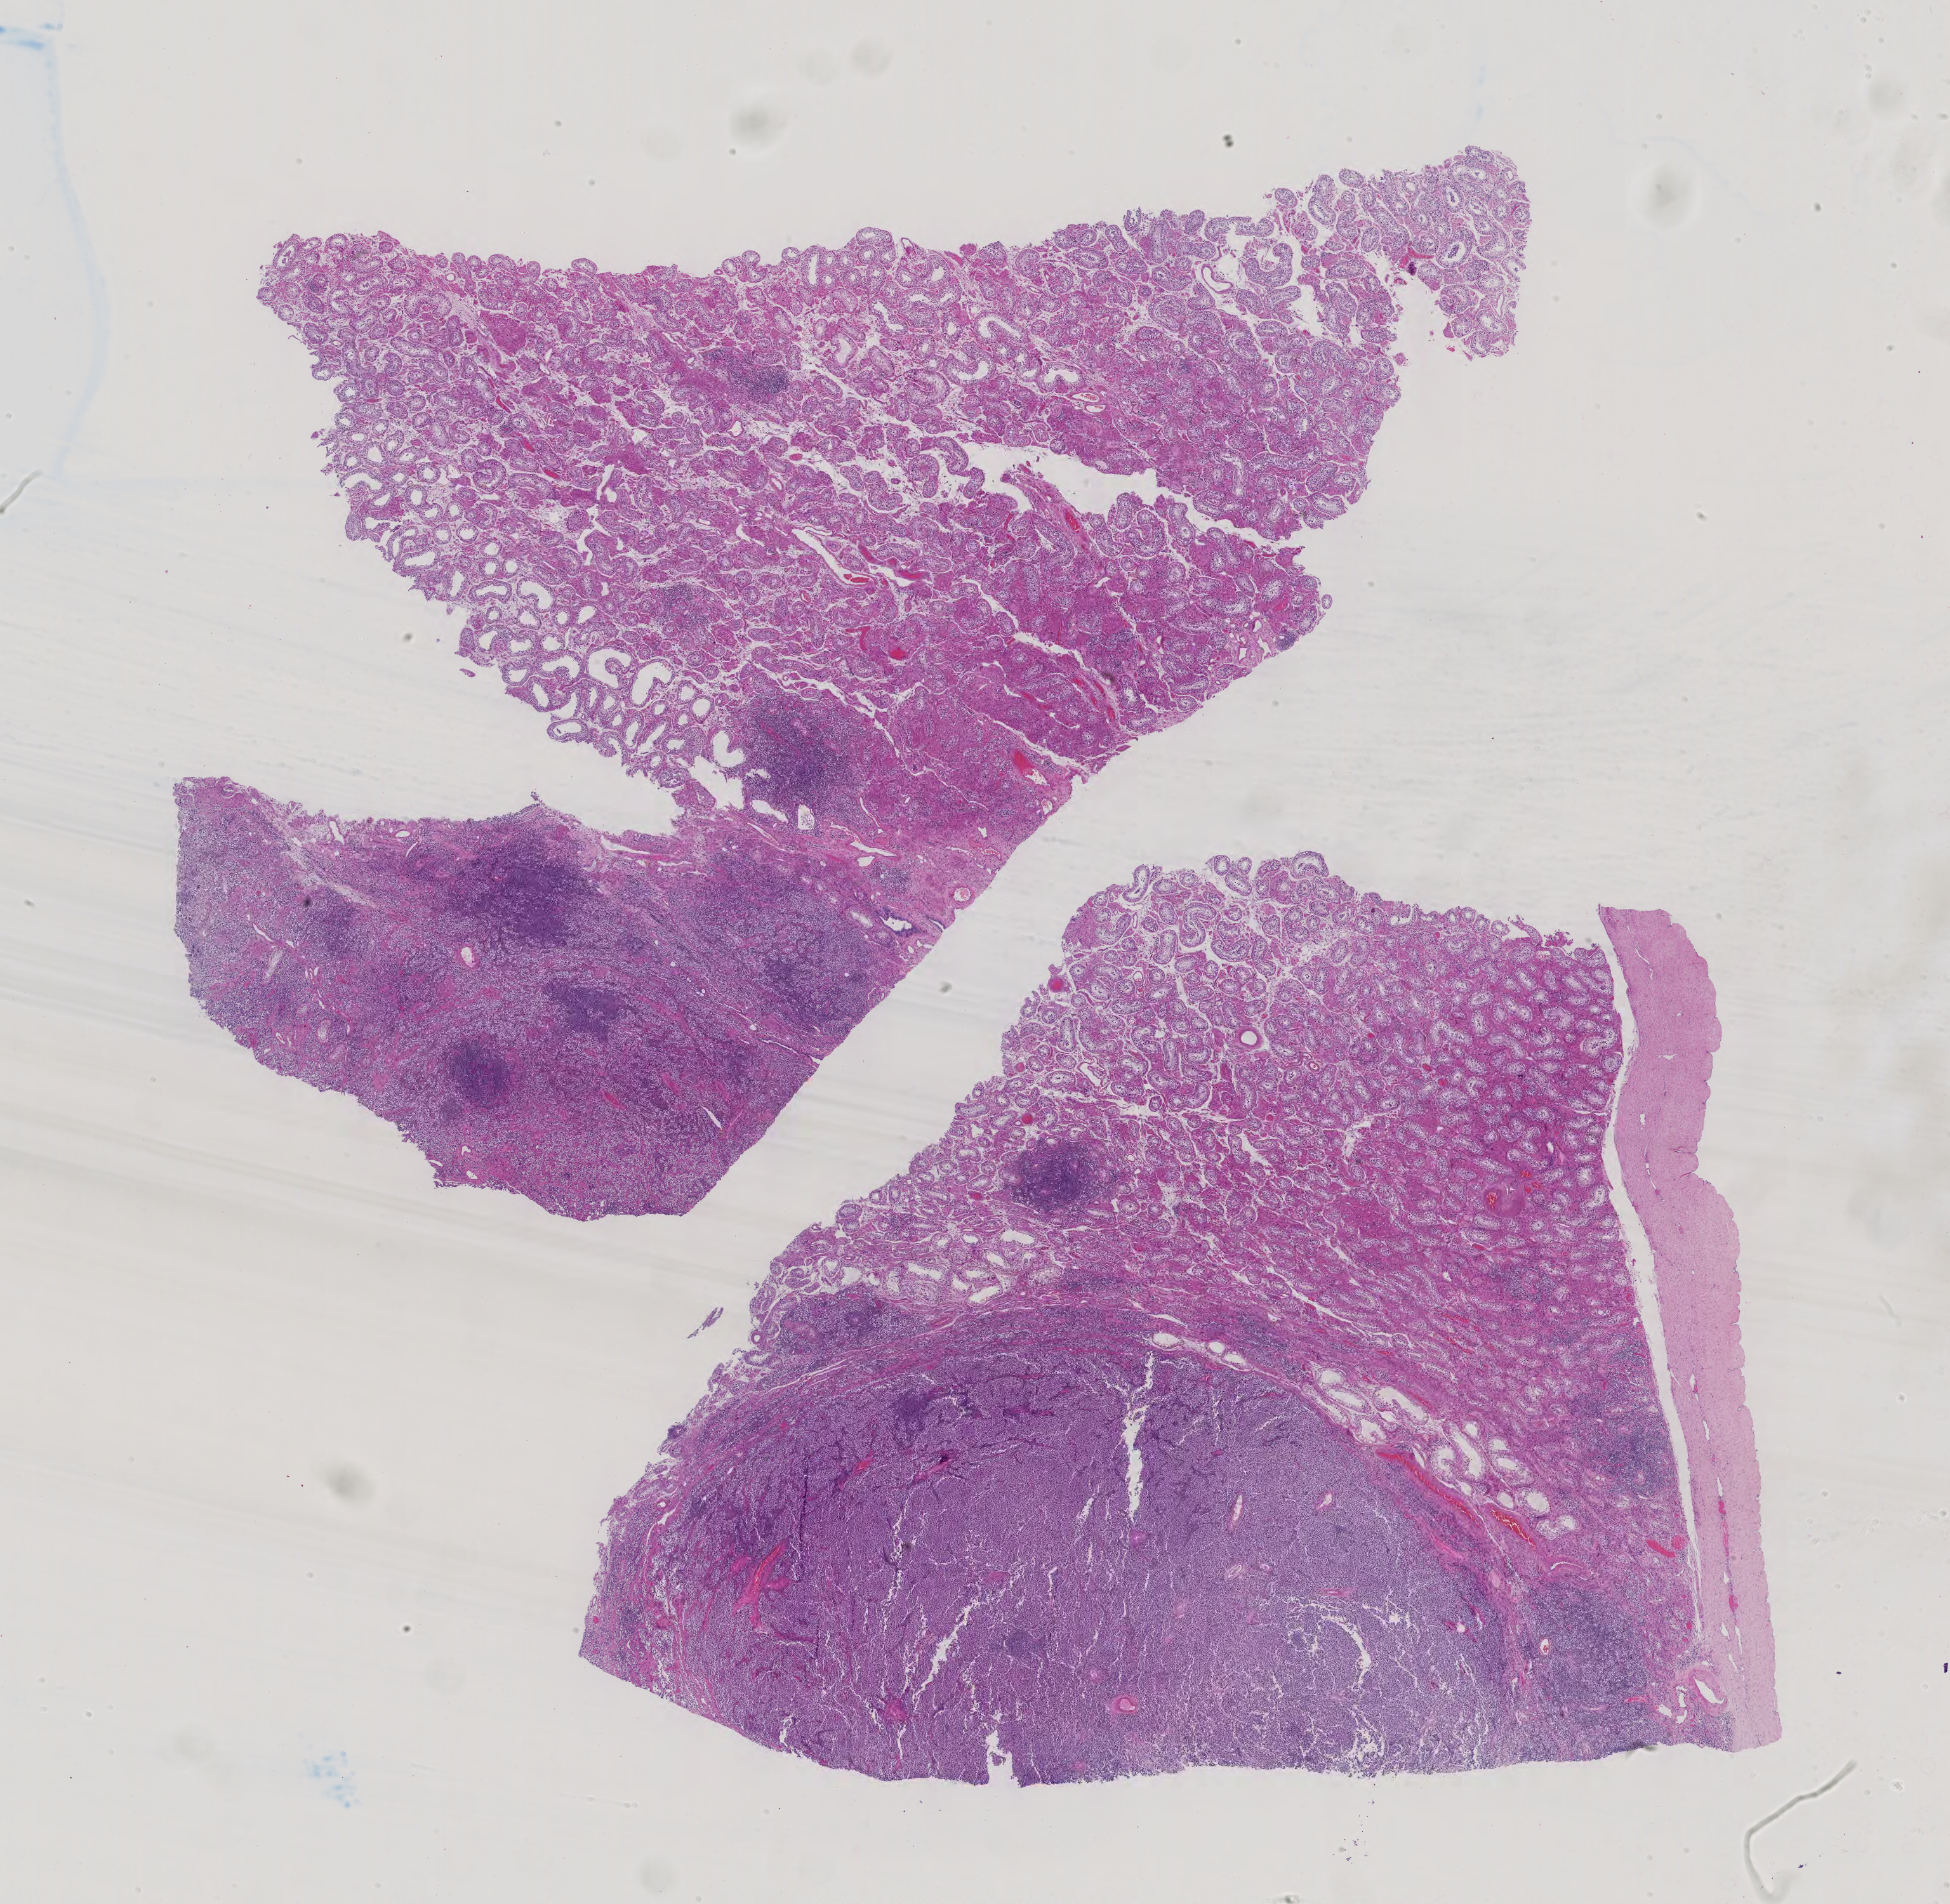
Digitized H&E tissue section (whole slide) — shown as a low-resolution overview of the whole scanned area (about 22.4 x 21.9 mm, acquisition: 40x scan), formalin-fixed paraffin-embedded (FFPE) diagnostic section, testis, additional new primary tumour sample. Patient: male, age at initial diagnosis 33 years.
This section: additional new primary tumour. Patient diagnosis: Mixed germ cell tumor.